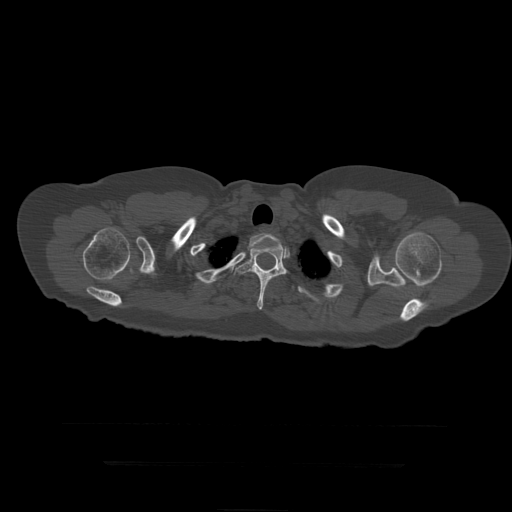
CT including the spine, one axial slice; position 365 of 399 along the scan axis; reconstruction kernel STANDARD; 120 kVp; bone window (W 1800 / L 400 HU); 1.25 mm slice thickness; 512 × 512 image matrix, field of view 450 × 450 mm. Patient age 41 years. From the clinical record (not read from this slice): primary cancer: breast.
Structures marked on this image (semi-automatic segmentation, software-assisted and operator-edited):
- T2 vertebra: bounding box <249,233,283,250> (left, top, right, bottom; pixels)
- T3 vertebra: <234,241,289,310>